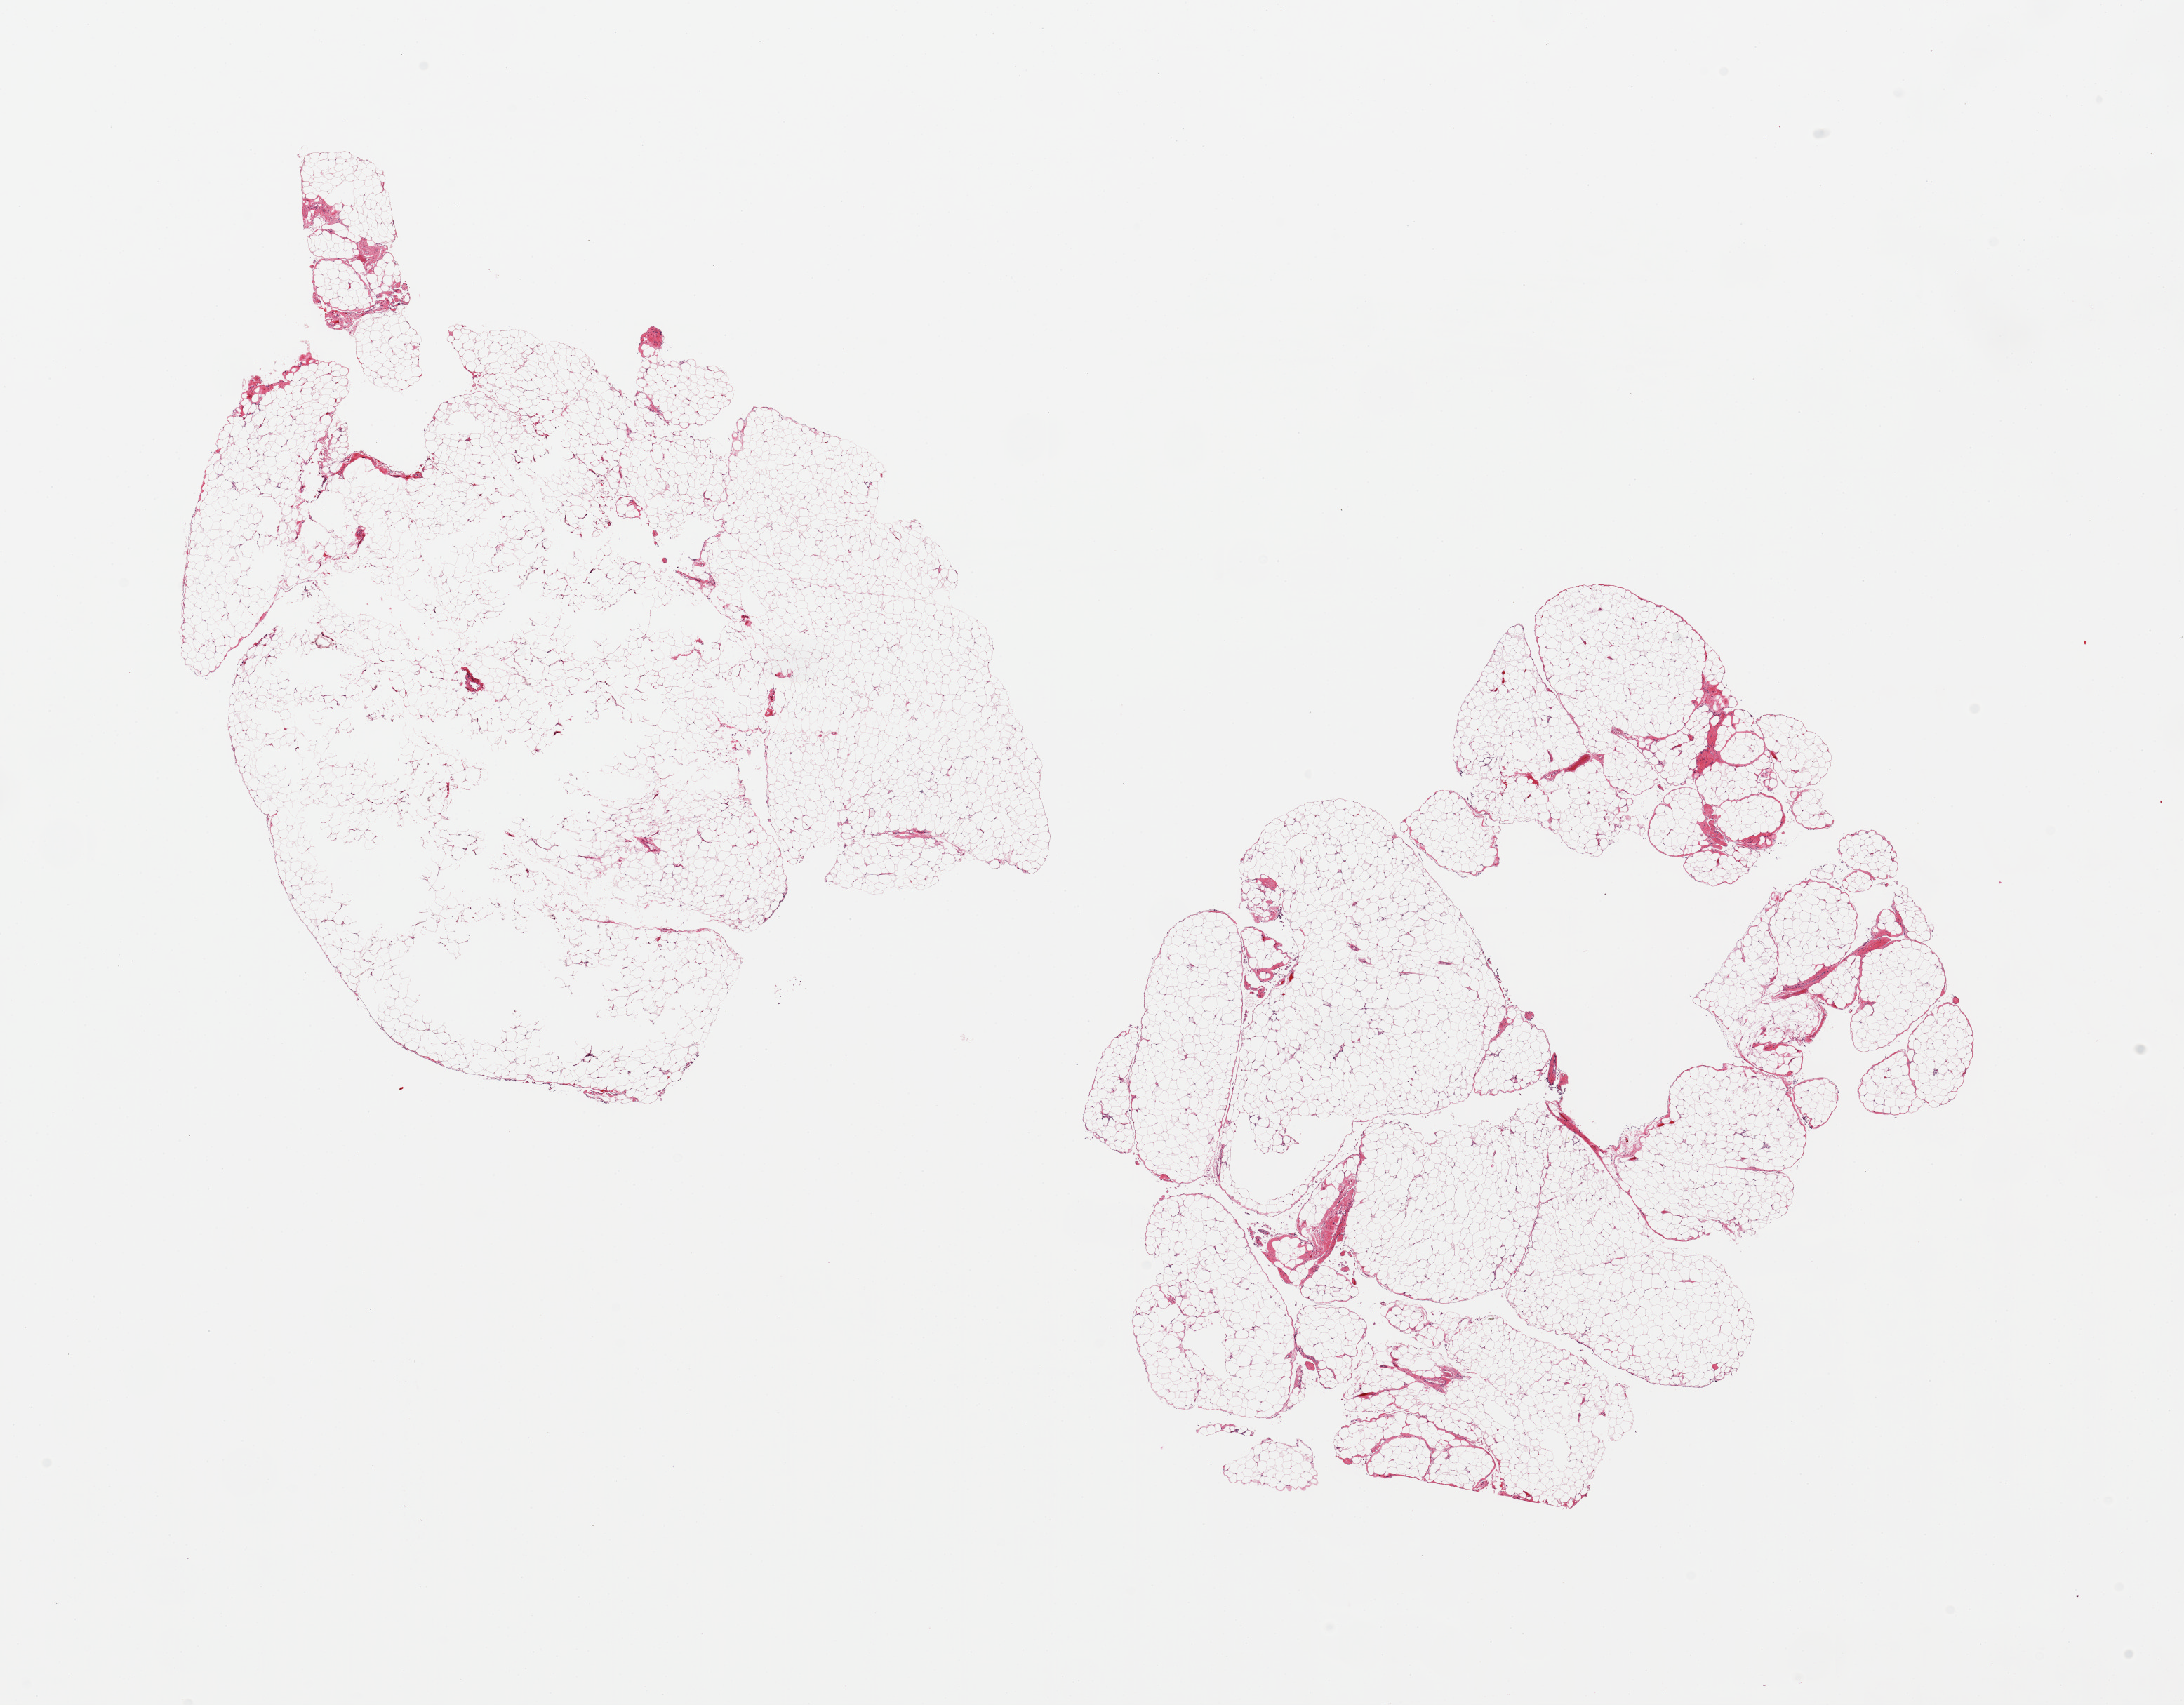
Digitized haematoxylin and eosin-stained section, brightfield — whole scanned area (about 24.6 x 19.2 mm, acquisition: 20x scan) shown as a low-resolution overview, PAXgene-fixed paraffin-embedded (PFPE) section, section of omentum (target tissue), tissue donor sample. Donor: male.
Pathologist's review note for this sample: 2 pieces; few central holes in one piece (?poor fixation).